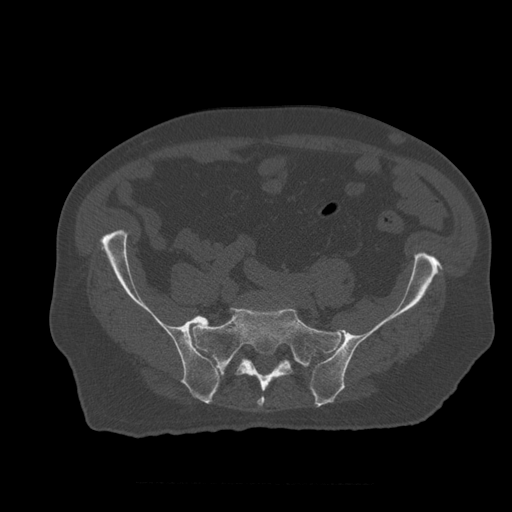
CT including the spine, one axial slice. Slice 119 of 399 in the series (ordered by position). Reconstruction kernel STANDARD. Bone window (W 1800 / L 400 HU). 1.25 mm slice thickness. 512 × 512 image matrix. Patient age 73 years. Case-level facts recorded for this patient, not image findings: primary cancer: prostate.
Outlined on this slice (semi-automatic segmentation, software-assisted and operator-edited):
- L5 vertebra: bounding box [x1, y1, x2, y2] px = [213, 363, 221, 376]